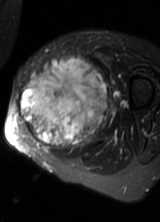
MRI of an extremity soft-tissue mass, one axial slice. Slice 30 of 69 in the series (ordered by position). T2-weighted fat-saturated. MR volume resampled by the dataset authors to the PET/CT grid (not the native acquisition matrix). 160 × 222 image matrix, field of view 156 × 217 mm. Female patient. Case-level facts recorded for this patient, not image findings: histological type: pleomorphic leiomyosarcoma; grade: high; site of the primary tumour: left thigh.
Structures marked on this image (expert contour drawn on MRI and transferred to this co-registered scan by the dataset authors):
- gross tumour volume including surrounding oedema: bounding box (x1, y1, x2, y2) in pixels: (18, 59, 108, 151)
- gross tumour volume (mass): (18, 59, 108, 149)